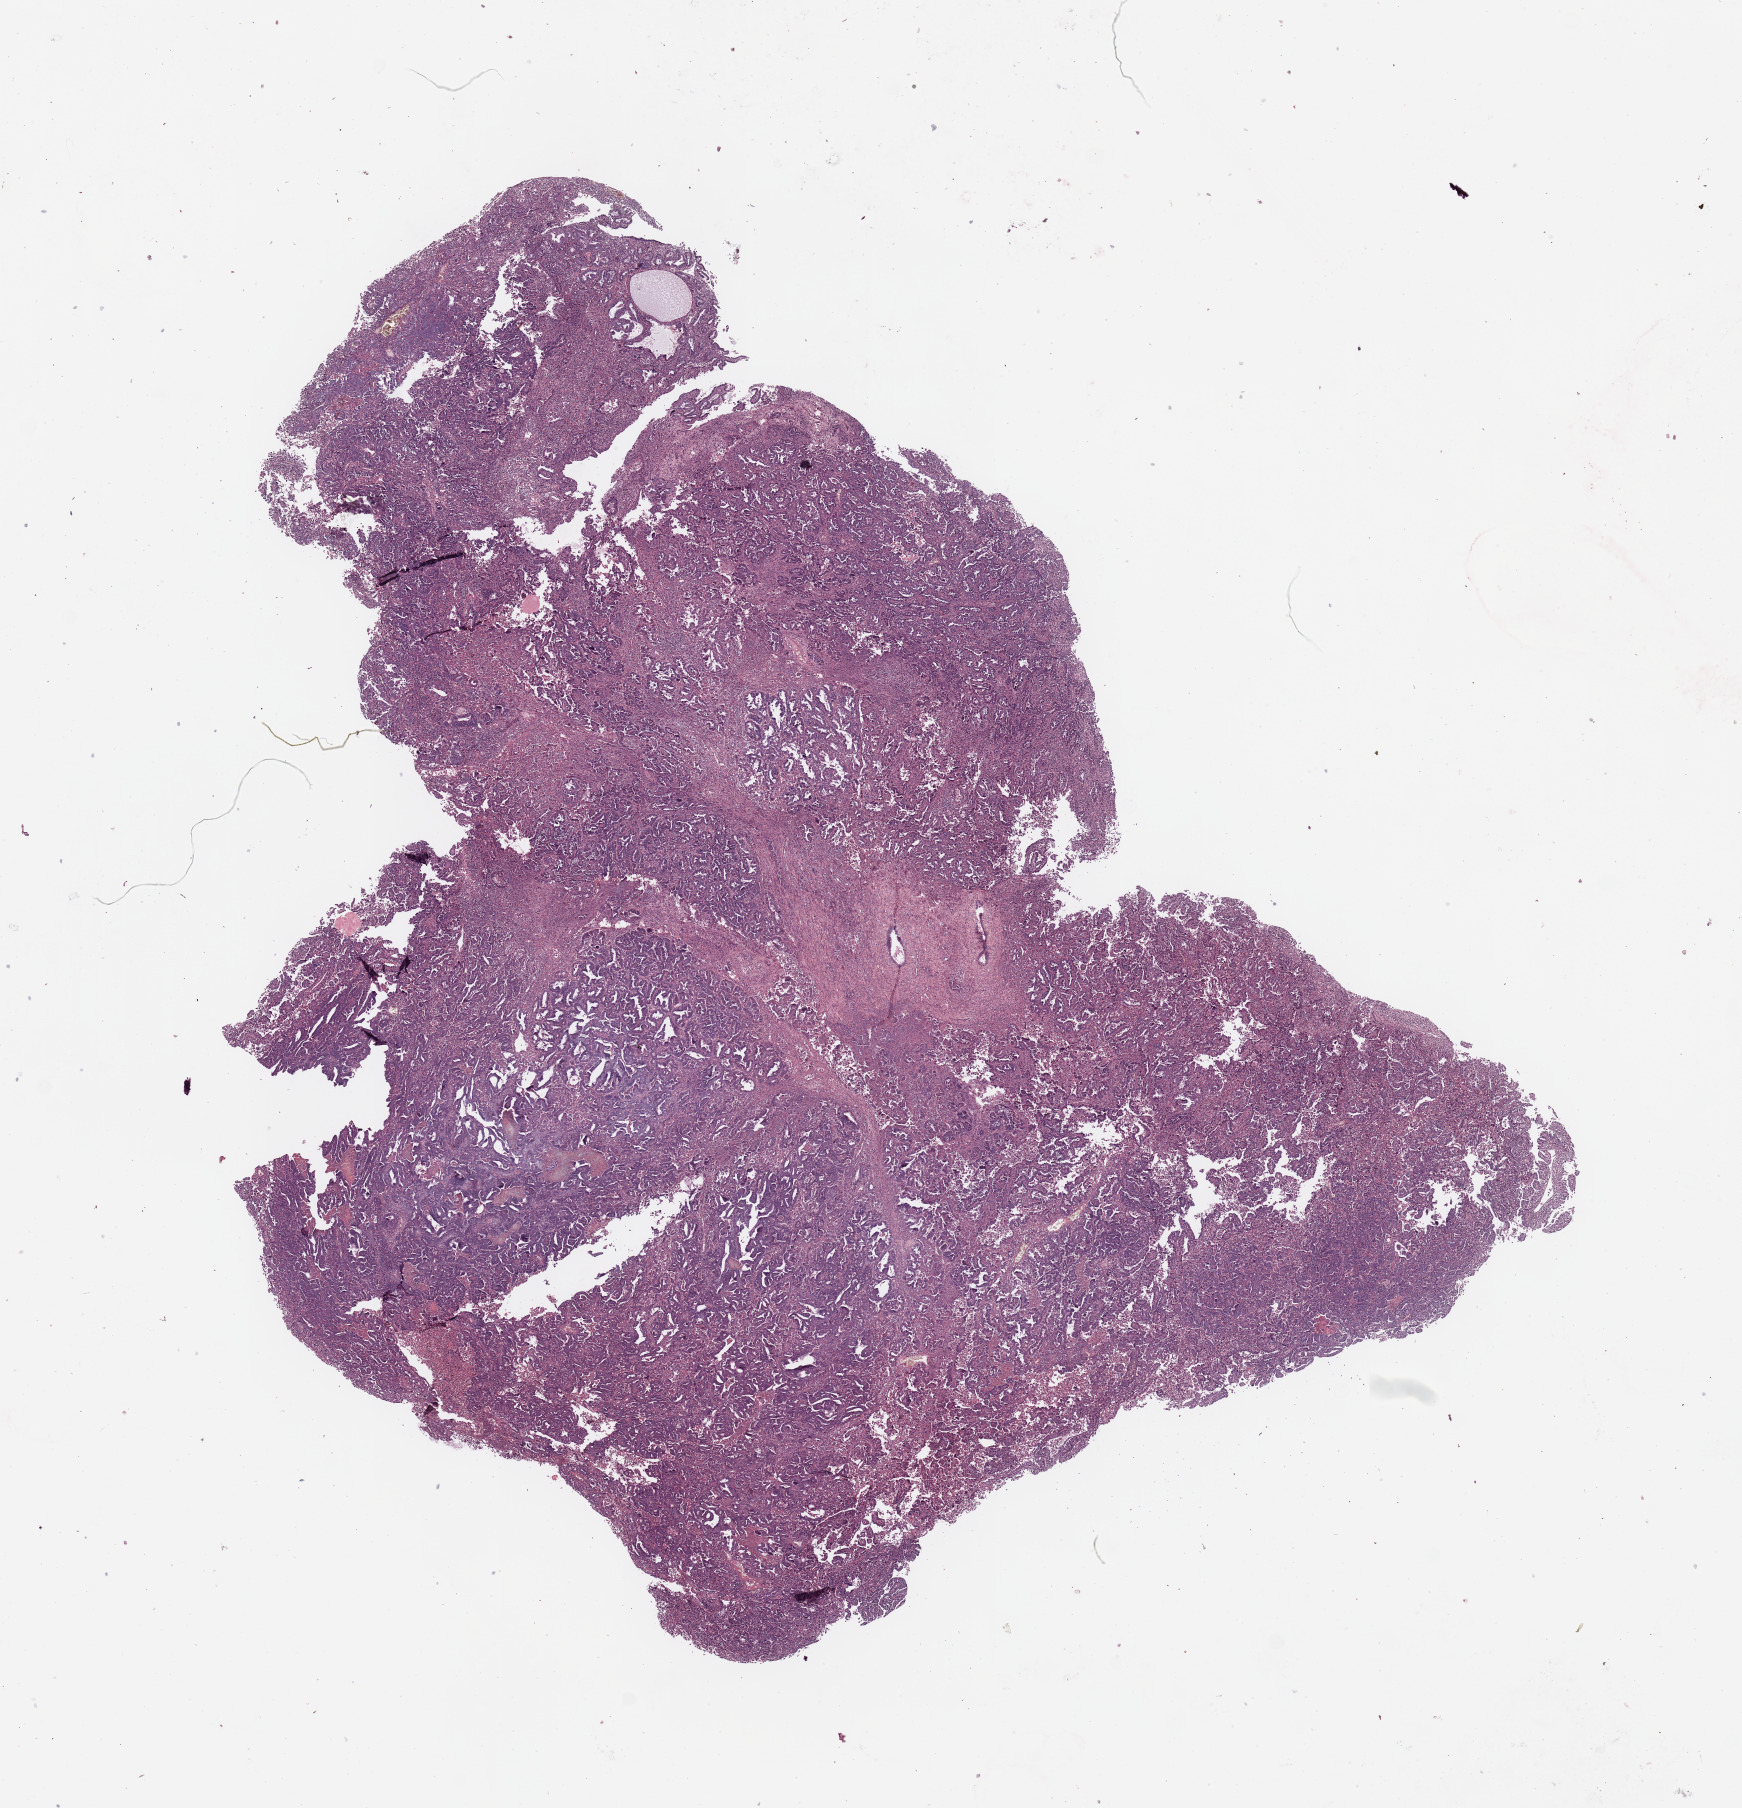
H&E whole-slide image — shown as a low-resolution overview of the whole scanned area (about 13.8 x 14.3 mm). Uterus, tumour tissue. 74-year-old female patient. Histologic grade: G3 (poorly differentiated).
Histologic diagnosis: Endometrioid adenocarcinoma, NOS. AJCC pathologic stage: II.